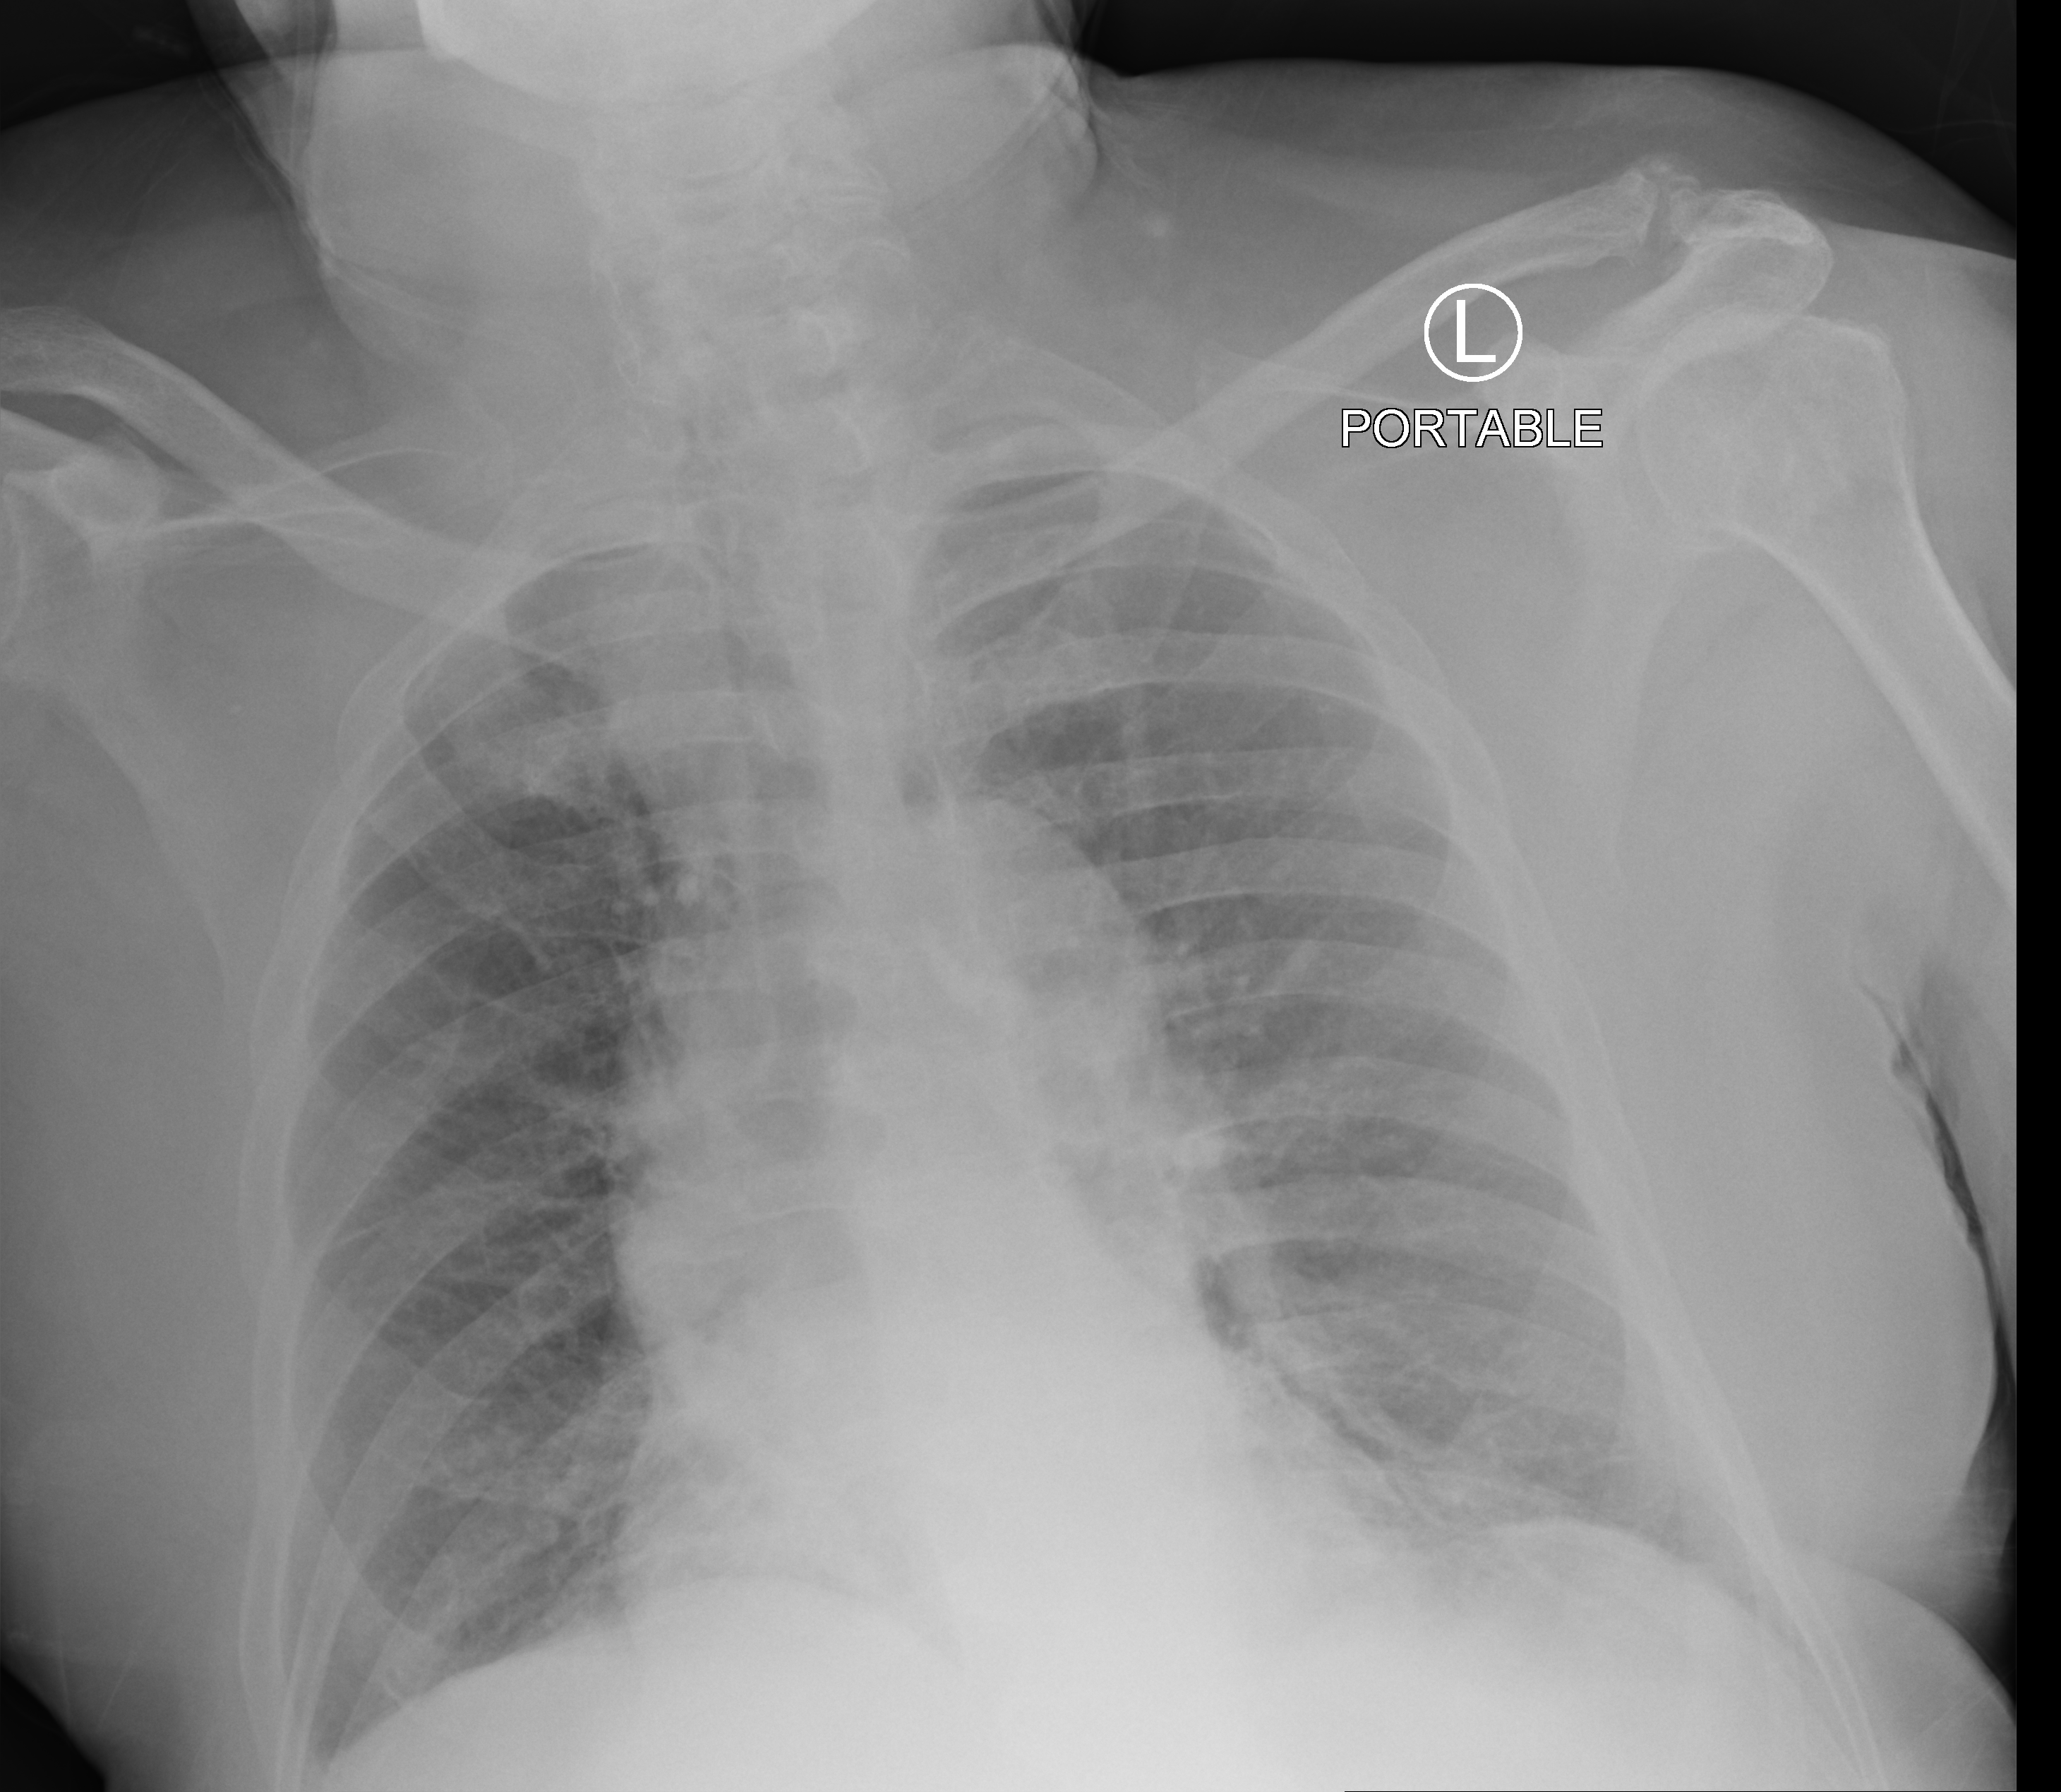
Chest X-ray (portable), anteroposterior (AP) projection. Patient hospitalised with COVID-19; male, aged 75–90 years.
From the hospital-stay record, not from the radiograph (when in the stay this image was taken is not recorded): mechanically ventilated during this hospital stay: no.